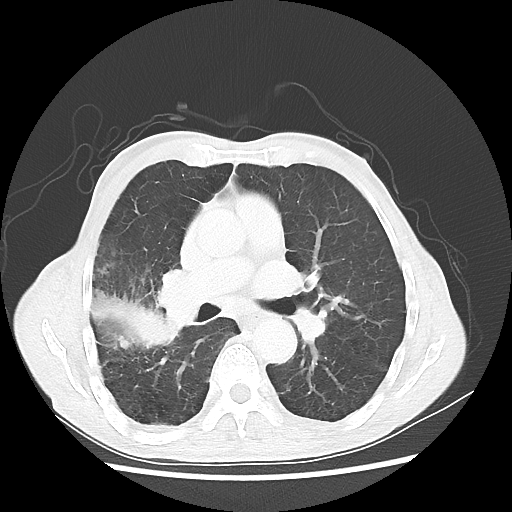
Chest CT, one axial slice. Slice 29 of 58 in the series (ordered by position). Reconstruction kernel LUNG. Lung window (W 1500 / L -600 HU). 5 mm slice thickness. 512 × 512 image matrix, field of view 351 × 351 mm. Patient: male, 75 years. From the clinical record (not read from this slice): clinical TNM (as recorded): T4 N1 M1.
Annotated regions visible in this slice (bounding box drawn by a radiologist):
- lung tumour (recorded histology: adenocarcinoma): bounding box (x1, y1, x2, y2) in pixels: (81, 283, 176, 351)